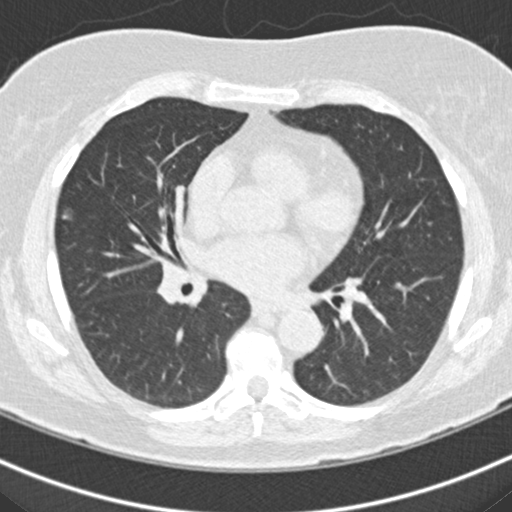
Low-dose screening chest CT, one axial slice; slice 97 of 160 in the series (ordered by position); 120 kVp; lung window (W 1500 / L -600 HU); 2 mm slice thickness; 512 × 512 image matrix.
Outlined on this slice (manually delineated by an expert):
- lesion 1 (tumor, middle lobe of right lung): bounding box [x1, y1, x2, y2] px = [63, 216, 66, 218]